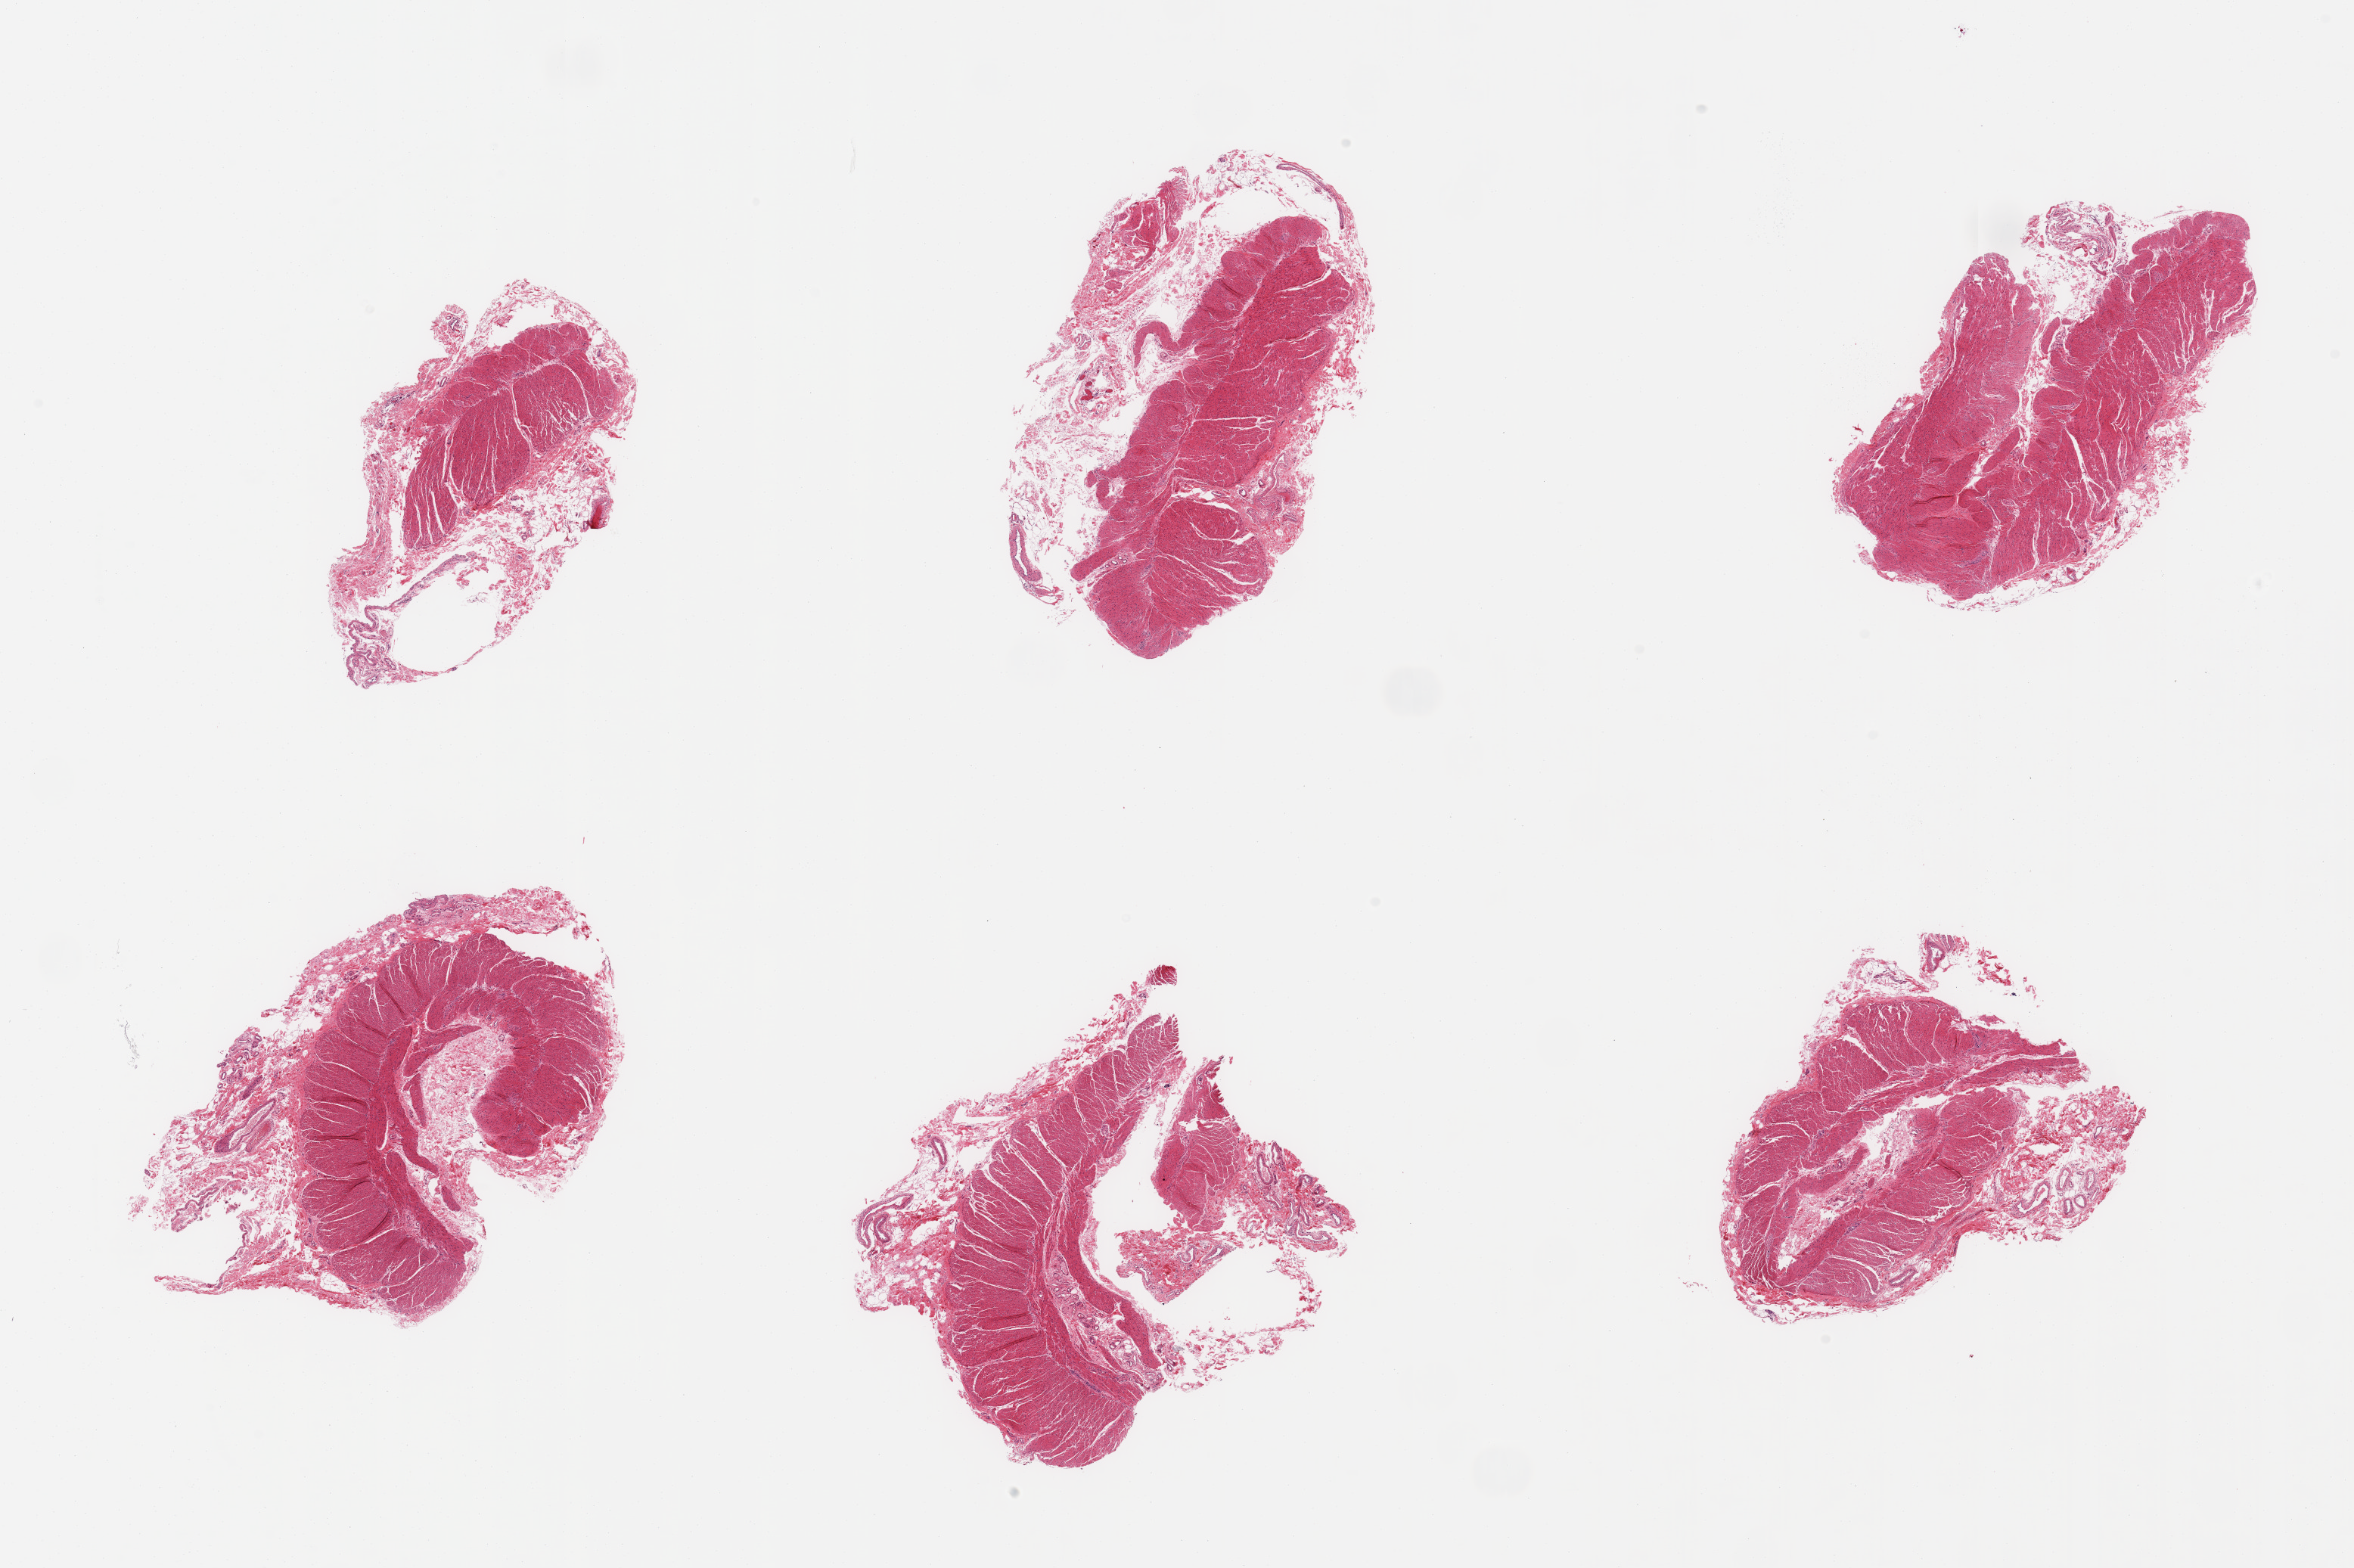
Whole-slide image, haematoxylin and eosin stain — whole scanned area (about 24.6 x 16.4 mm, slide scanned at 20x) shown as a low-resolution overview, PAXgene-fixed paraffin-embedded (PFPE) section, section of transverse colon (target tissue), tissue donor sample. Male donor.
* reviewer comment on this tissue sample: 6 pieces; target mucosa not present; muscularis only with up to 1.6mm adherent loose connective tissue